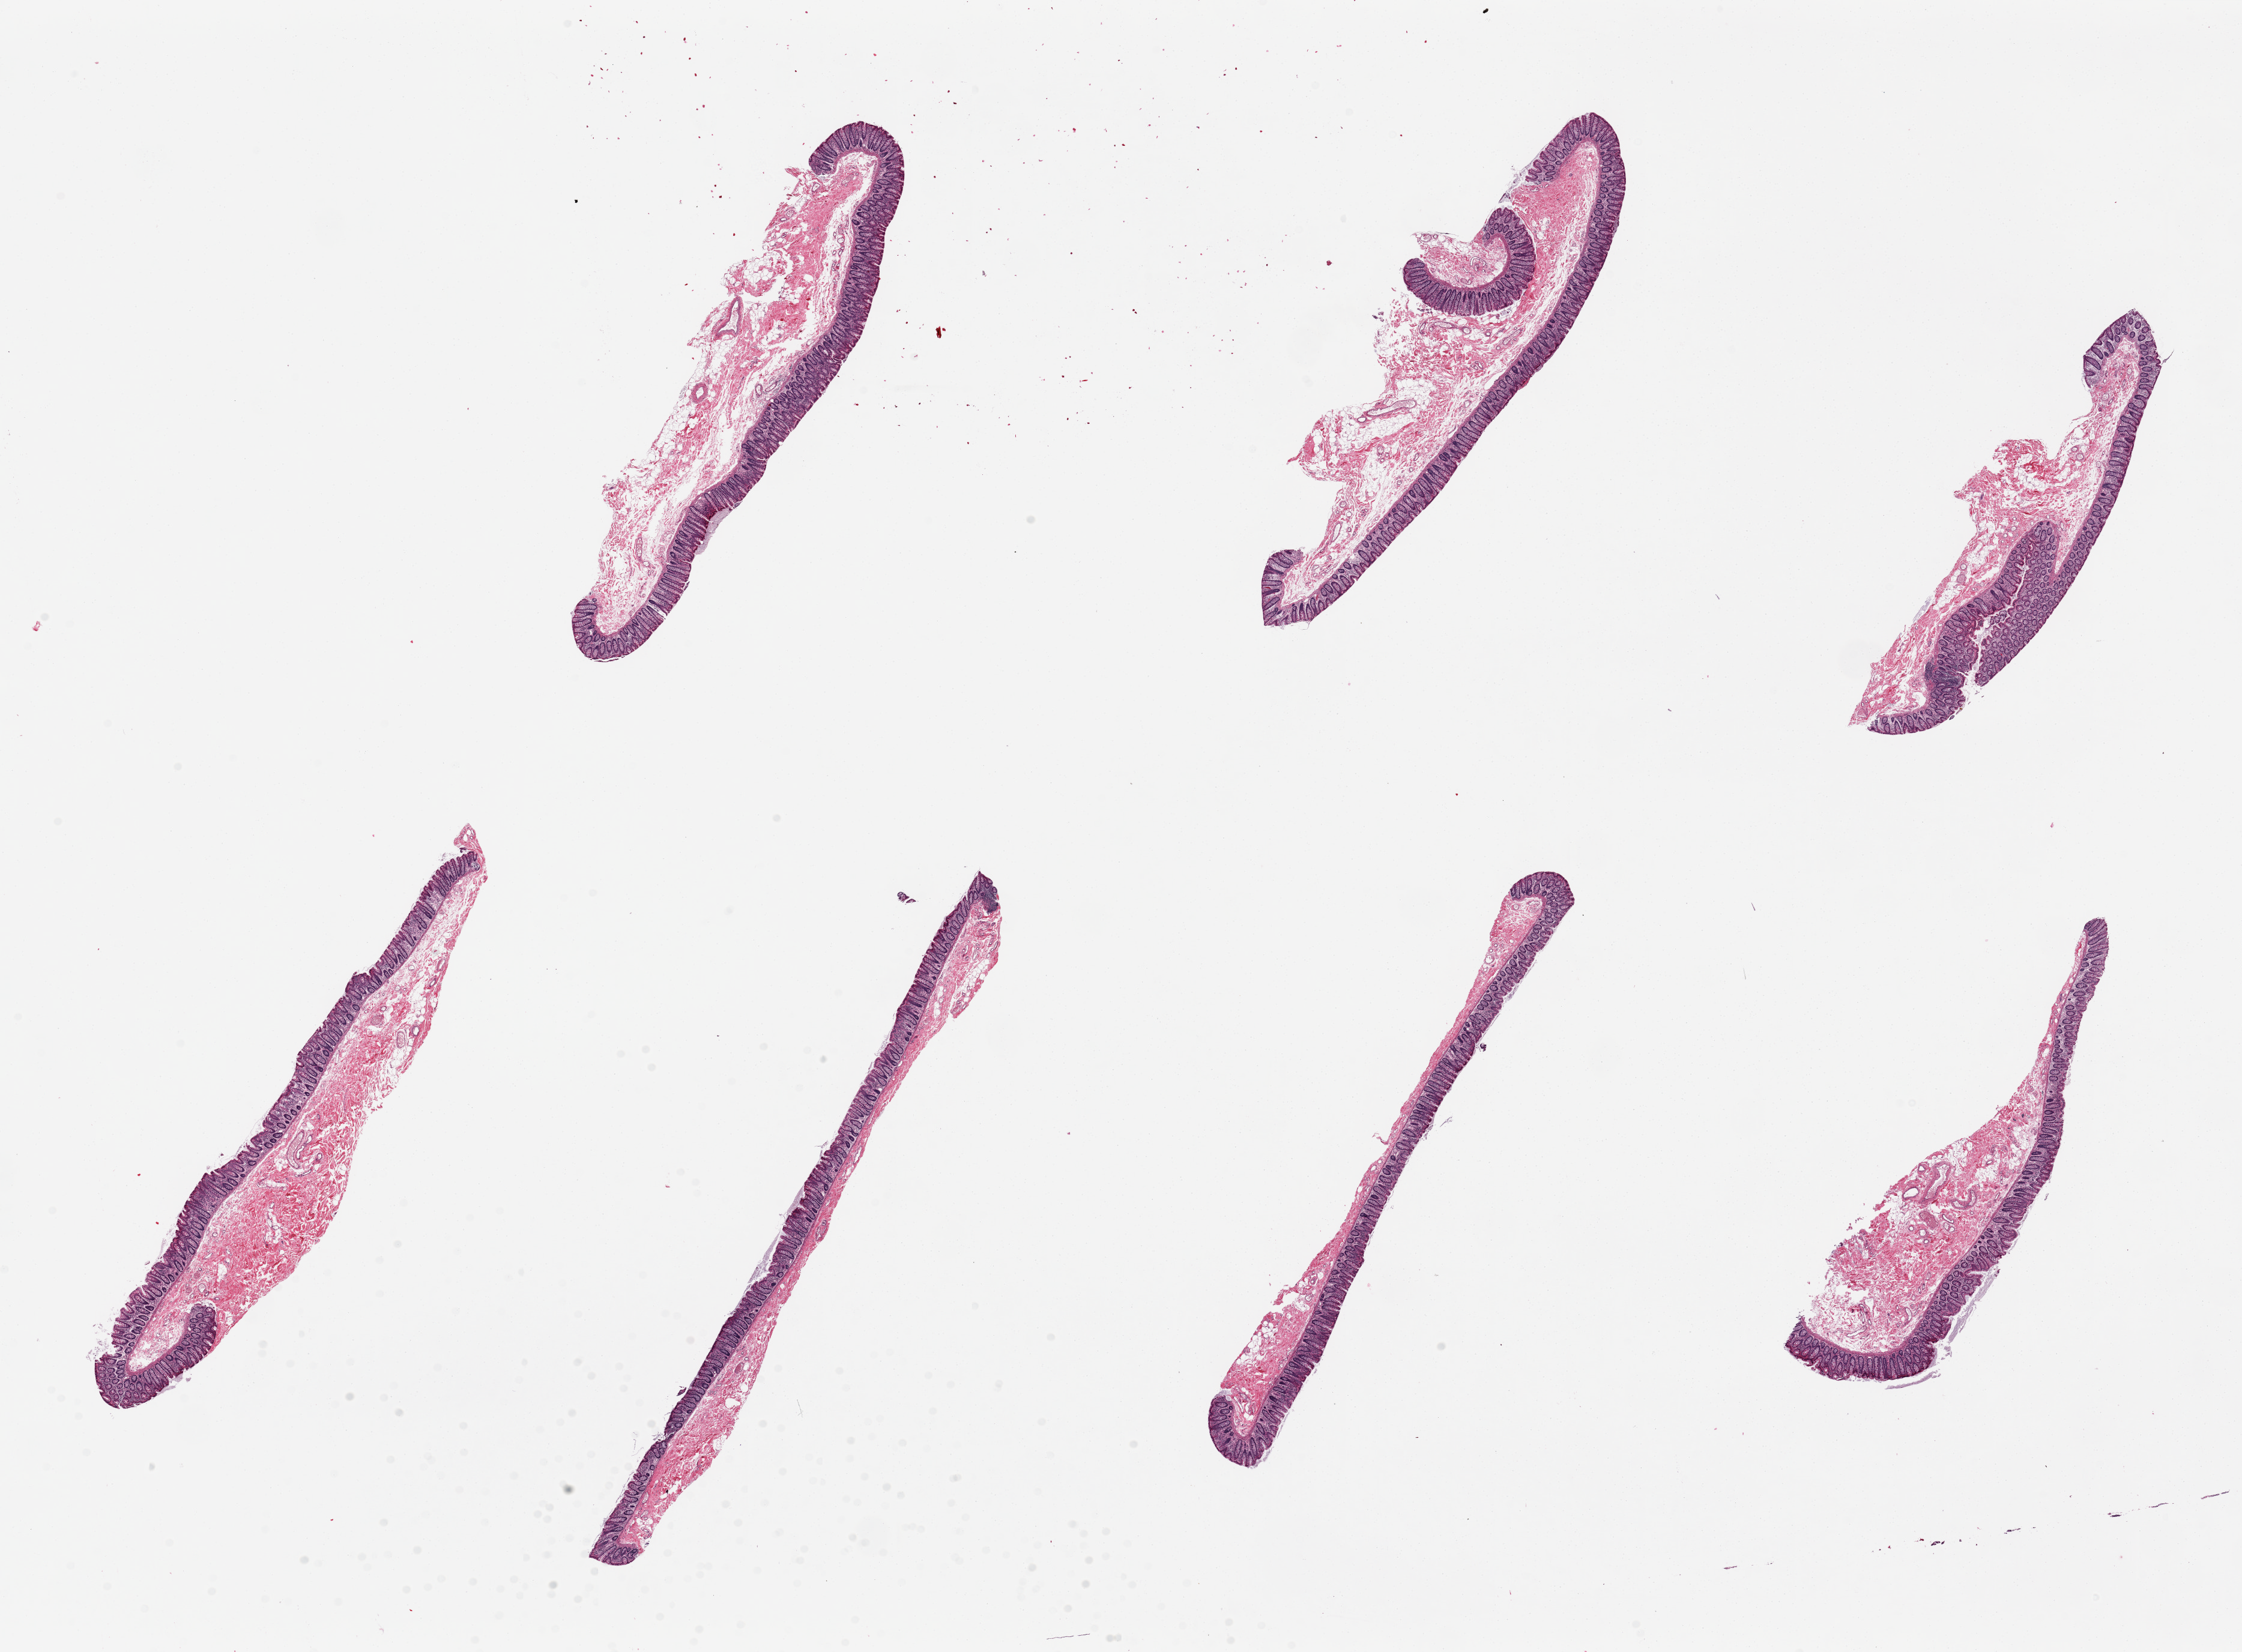
Whole-slide image, hematoxylin and eosin (H&E) stain — a low-resolution overview of the entire scanned area, about 29.5 x 21.8 mm (slide scanned at 20x). PAXgene-fixed, paraffin-embedded tissue. Section of transverse colon (target tissue). Tissue donor sample. Donor: male.
* pathologist's review note for this sample: 1 piece with small amount (1.6x0.8 mm) muscularis propria